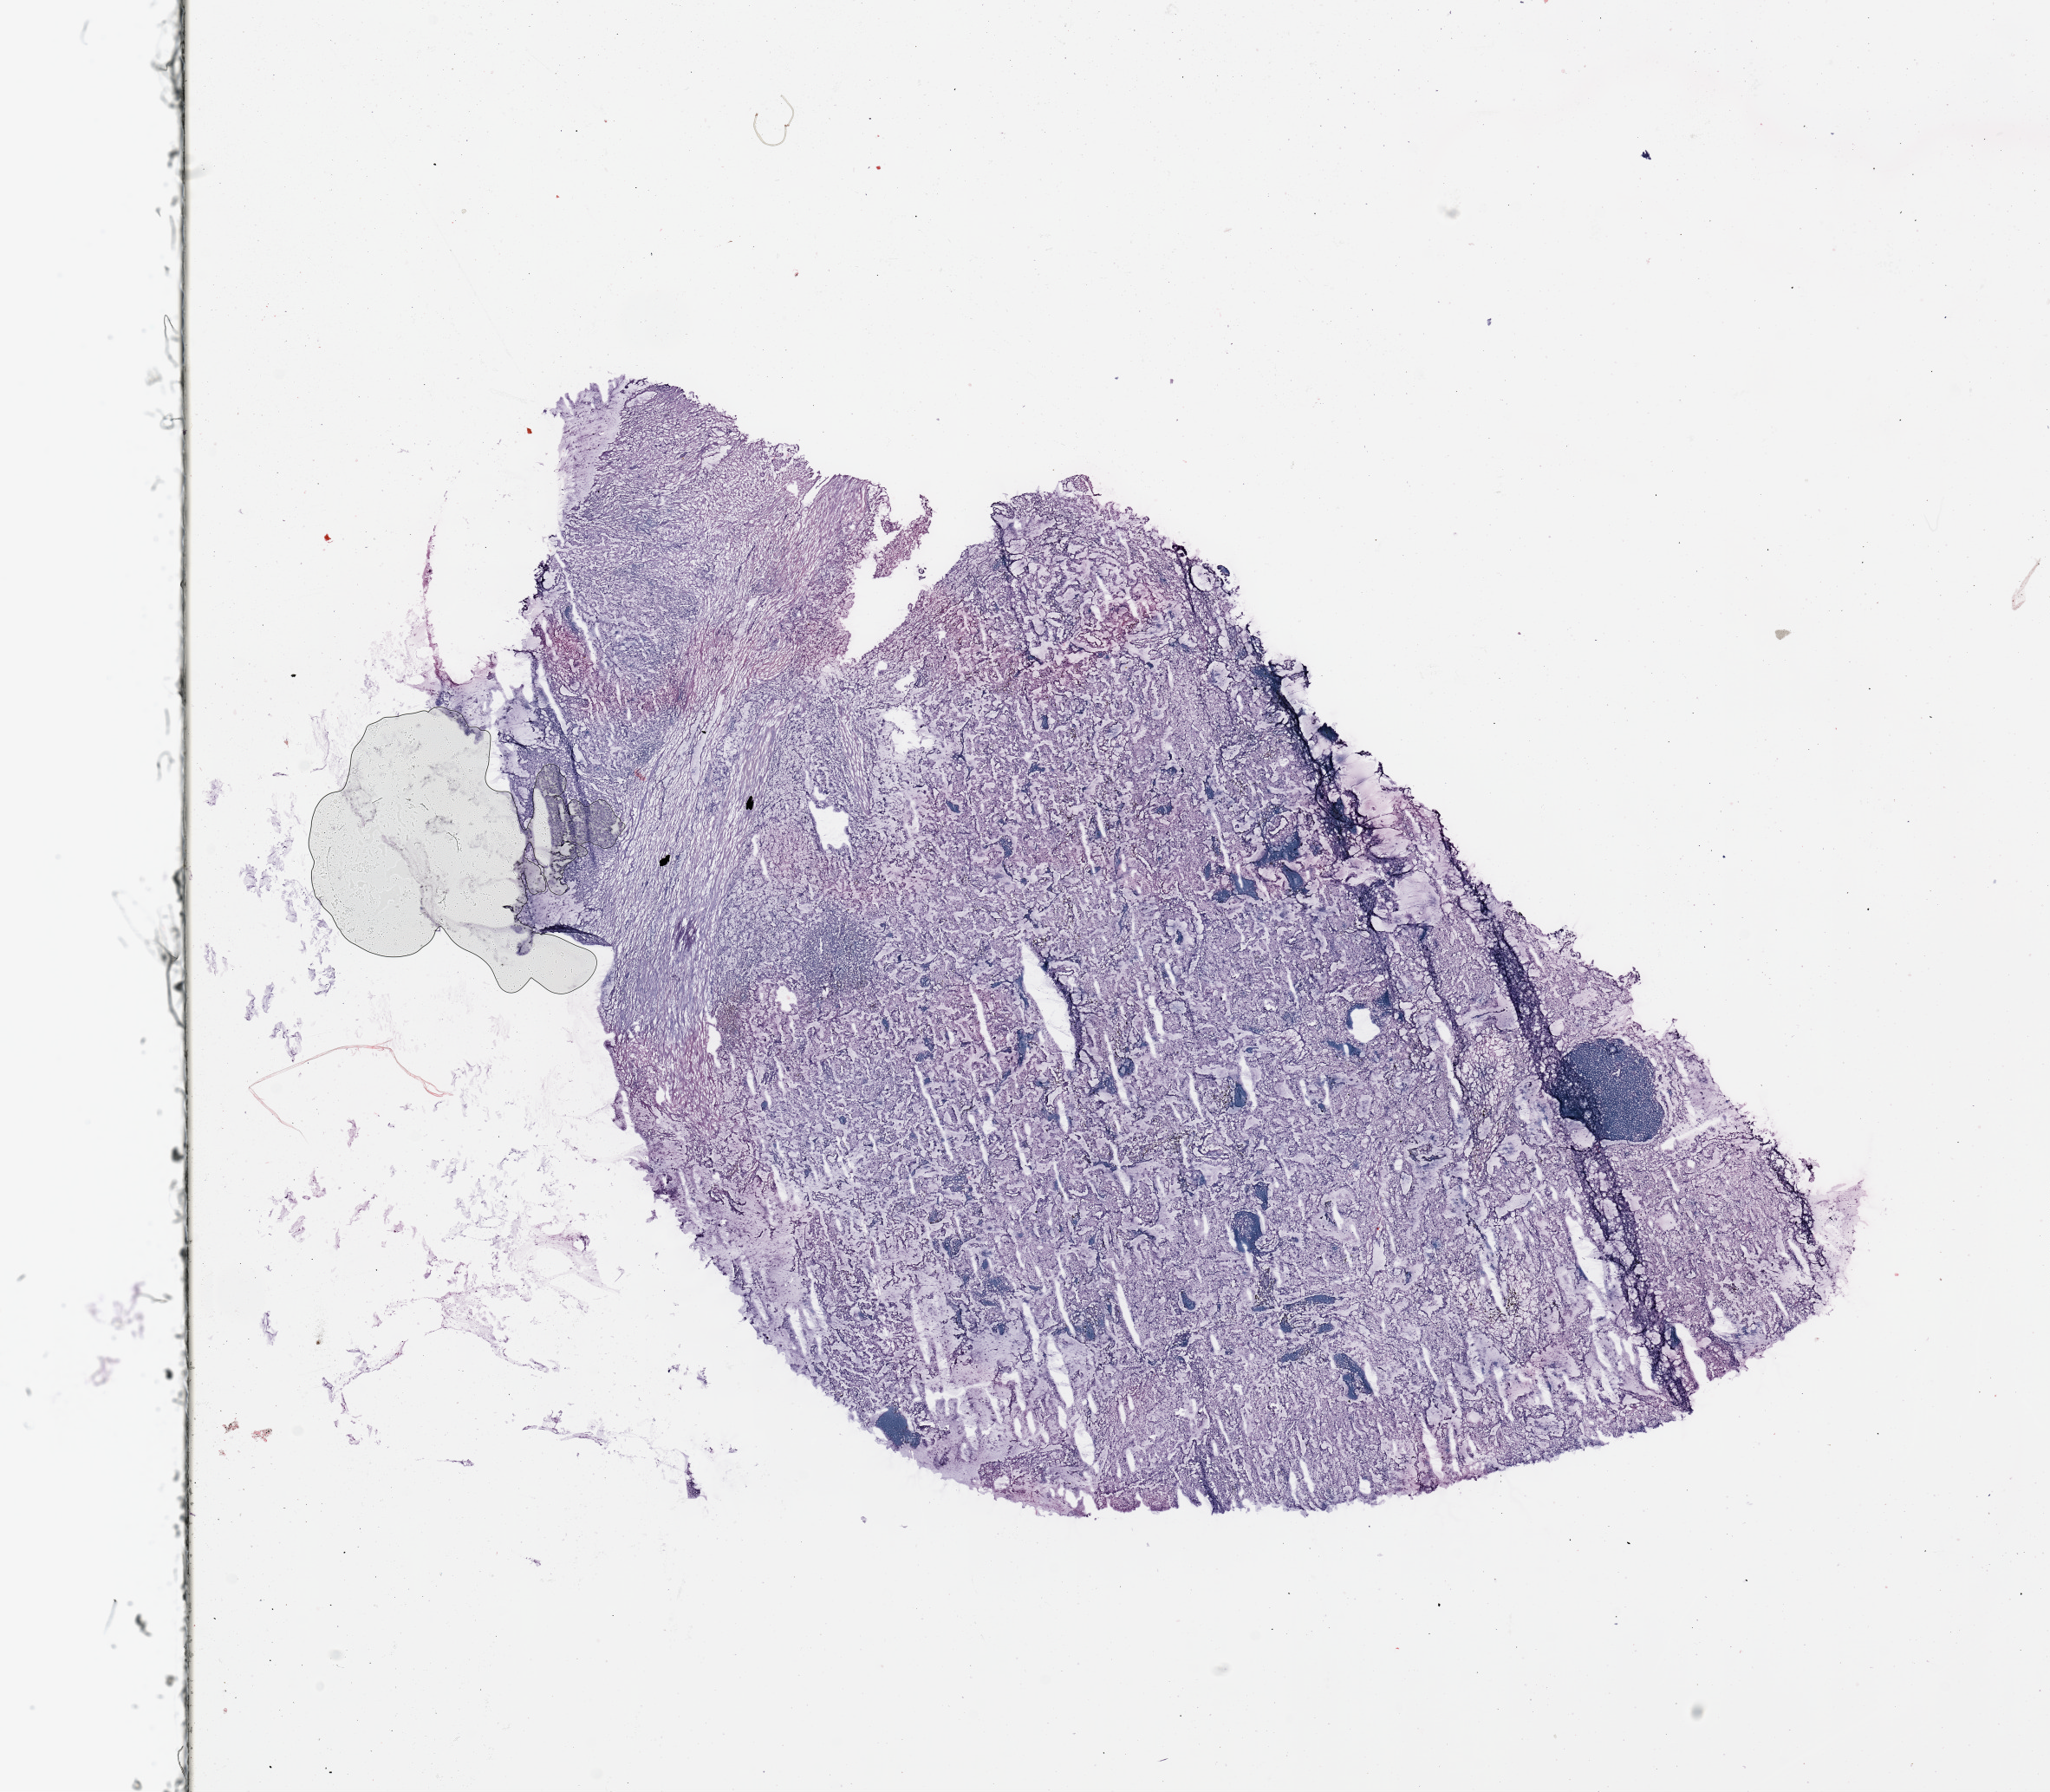
Whole-slide histology image, Hematoxylin and eosin (H&E) stained, whole scanned area (about 18.7 x 16.3 mm, from a 20x scan) shown as a low-resolution overview. Tumour tissue sample, kidney. 57-year-old female patient. Histologic grade: G2 (moderately differentiated).
* AJCC pathologic stage: I
* primary tumour site (as recorded): upper pole
* histologic diagnosis: Renal cell carcinoma, NOS